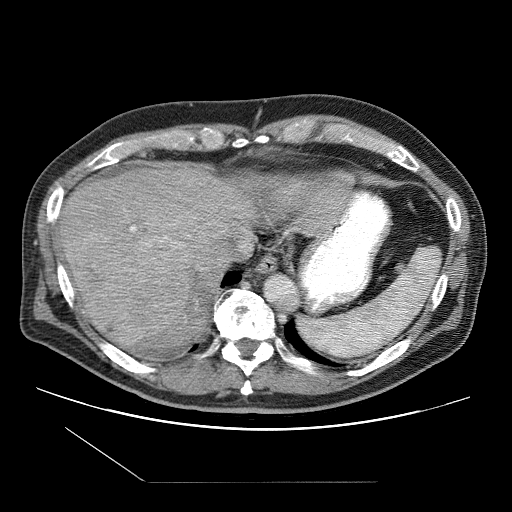
Contrast-enhanced abdominal CT (liver protocol), one axial slice; slice 83 of 109 in the series (ordered by position); 120 kVp; one of 2 acquisitions stored at this slice position; soft-tissue window (W 400 / L 40 HU); 2.5 mm slice thickness; 512 × 512 image matrix. From the clinical record (not read from this slice): diagnosis: hepatocellular carcinoma (patient treated with transarterial chemoembolisation; whether this scan precedes or follows treatment is not stated here); TNM stage (as recorded): Stage-IIIB; Child-Pugh class: A; tumour differentiation: well differentiated; tumour nodularity: multinodular.
Outlined on this slice (semi-automatic segmentation, software-assisted and operator-edited):
- liver parenchyma outside the tumour (the mass and vessels are separate outlines, so this box may not span the whole liver): bounding box <58,164,294,346> (left, top, right, bottom; pixels)
- mass: <61,222,192,342>
- liver vessels: <130,207,245,248>